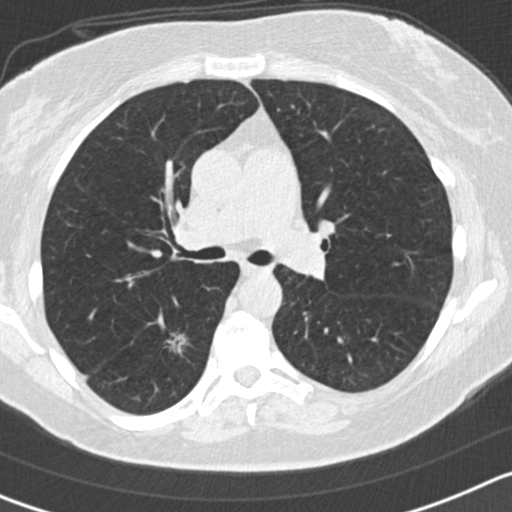
Chest CT (low-dose screening protocol), one axial image. First (baseline) screen. Lung window (W 1500 / L -600 HU). 120 kVp. Slice 63 of 161 in the series. Female participant, aged 65 years at enrolment. Former smoker at enrolment.
- Expert reader's lesion annotation, bounding box (x1, y1, x2, y2) in pixels: (142, 316, 199, 370).
- Reader record for this screening exam (exam-level; its link to the box is not recorded): non-calcified nodule or mass ≥4 mm, right lower lobe, 14 × 13 mm, spiculated (stellate) margins, mixed attenuation.